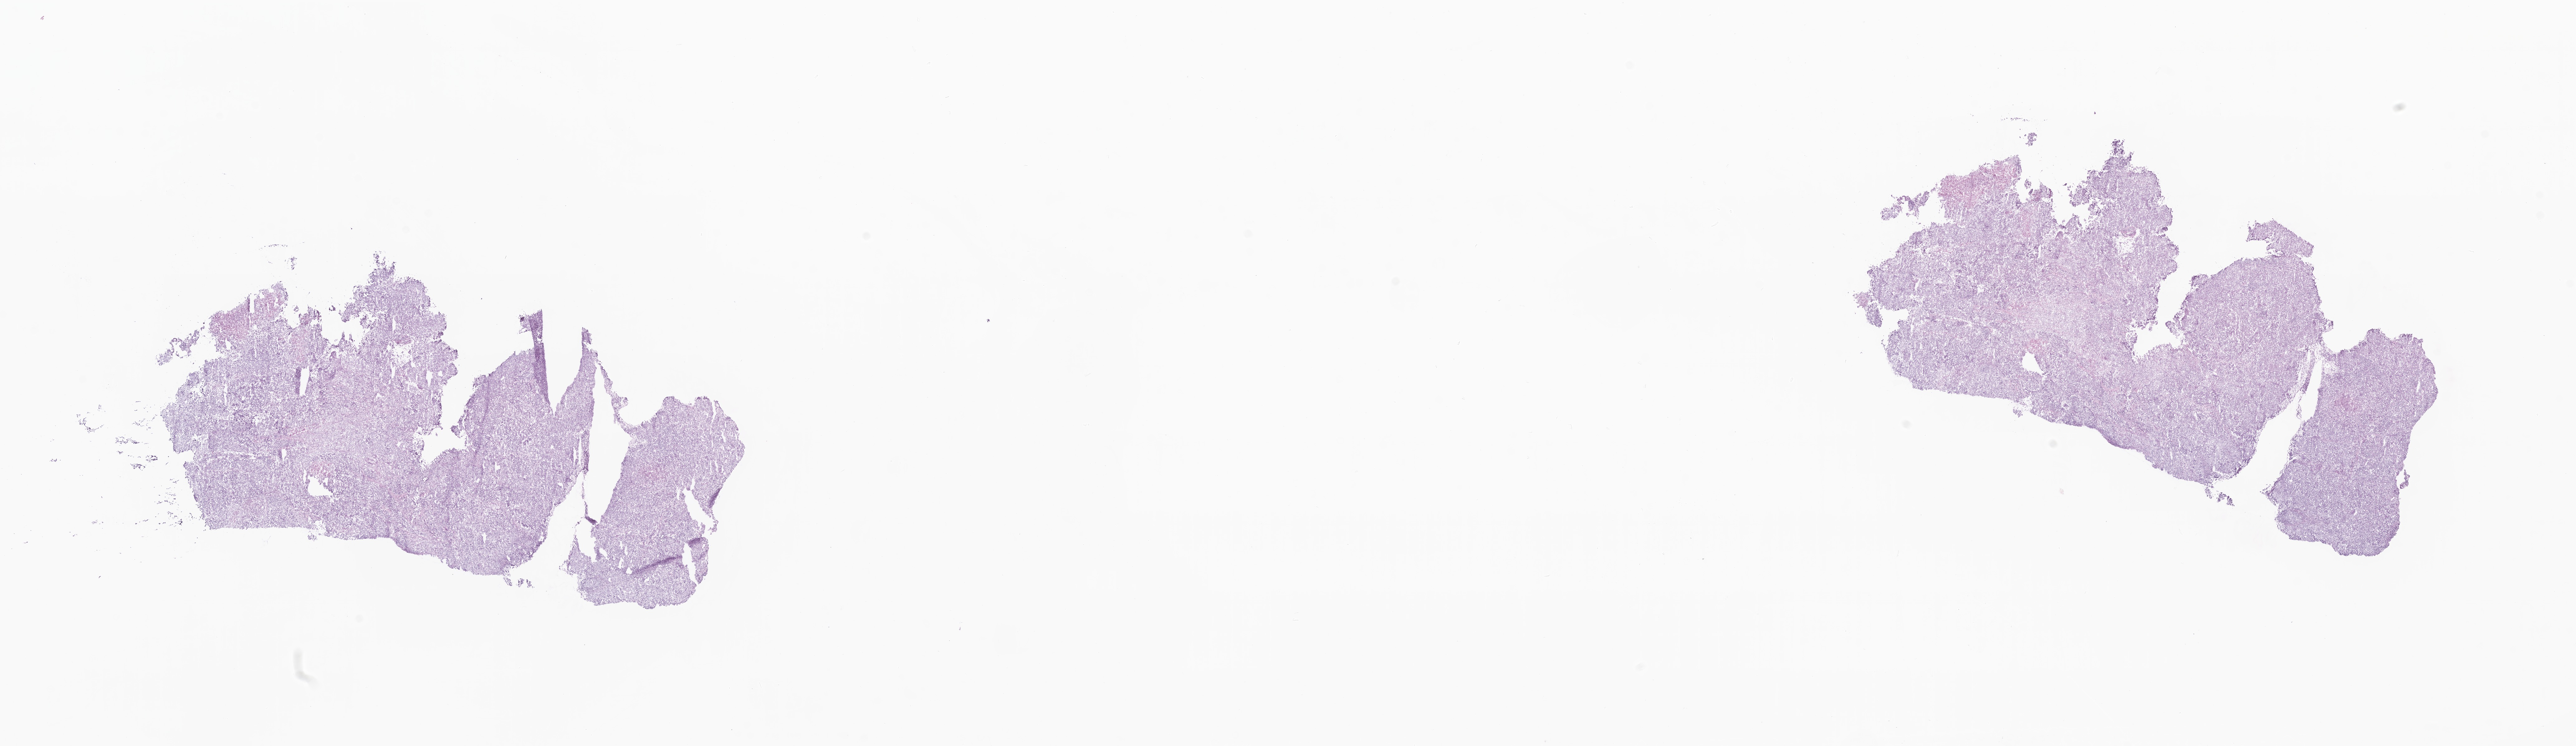
Whole-slide image, H&E stain — shown as a low-resolution overview of the whole scanned area (about 34.8 x 10.1 mm). Cryosection. Metastatic tumor tissue, resected from lymph node. Male, age 58 years at initial diagnosis. Pathologist review of this section (percent, as recorded): tumor cells 60%, tumor nuclei 69%, stromal cells 8%, necrosis 5%, normal cells 27%. Inflammatory infiltration, as recorded: lymphocyte infiltration 1%, monocyte infiltration 13%, neutrophil infiltration 9%.
Patient diagnosis (primary): Adenocarcinoma, metastatic, NOS.